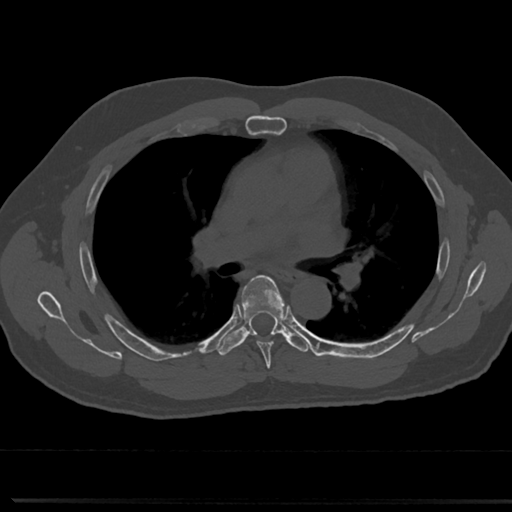
CT including the spine, one axial slice. Slice 472 of 817 in the series (ordered by position). 120 kVp. Bone window (W 1800 / L 400 HU). 512 × 512 image matrix, field of view 355 × 355 mm. Patient: male, 61 years. From the clinical record (not read from this slice): primary cancer: prostate.
Outlined on this slice (semi-automatic segmentation, software-assisted and operator-edited):
- T5 vertebra: bounding box [x1, y1, x2, y2] px = [241, 277, 287, 361]
- T6 vertebra: [220, 276, 286, 353]